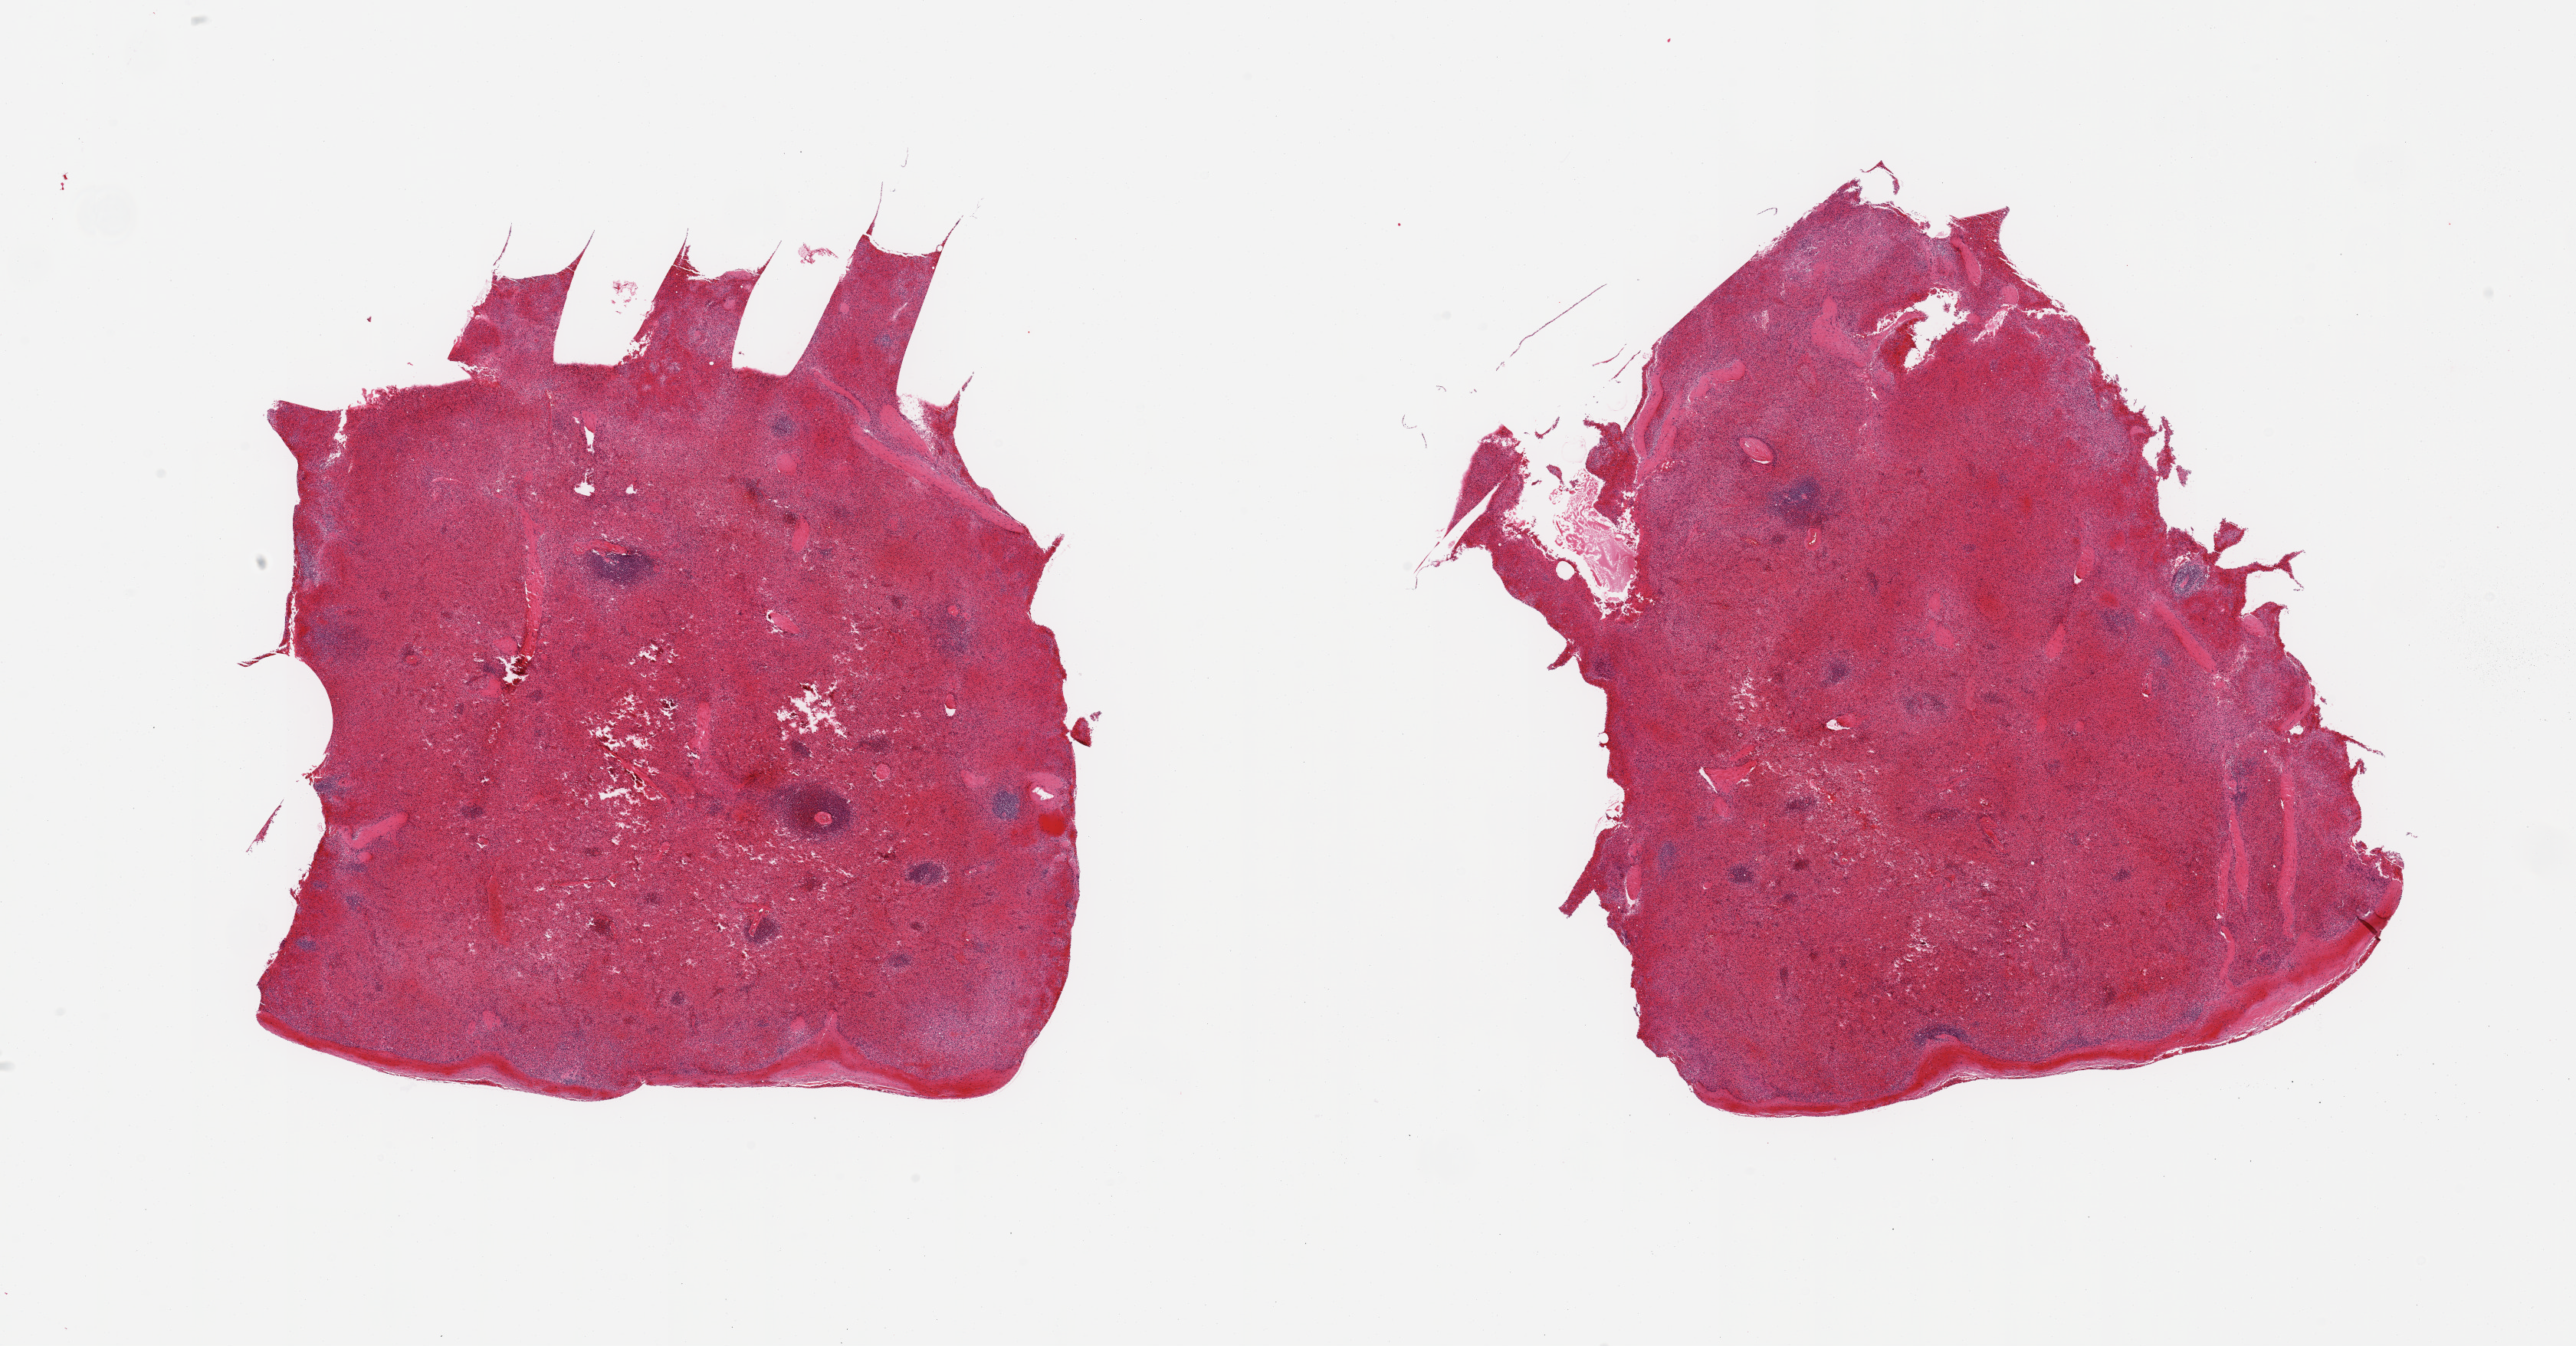
Whole-slide image, hematoxylin and eosin (H&E) stain, a low-resolution overview of the entire scanned area, about 26.6 x 13.9 mm (acquisition: 20x scan); PAXgene-fixed paraffin-embedded (PFPE) section; target tissue: spleen; donor tissue sample. Donor: male.
Reviewer comment on this tissue sample: 2 pieces, congested, advanced autolysis.